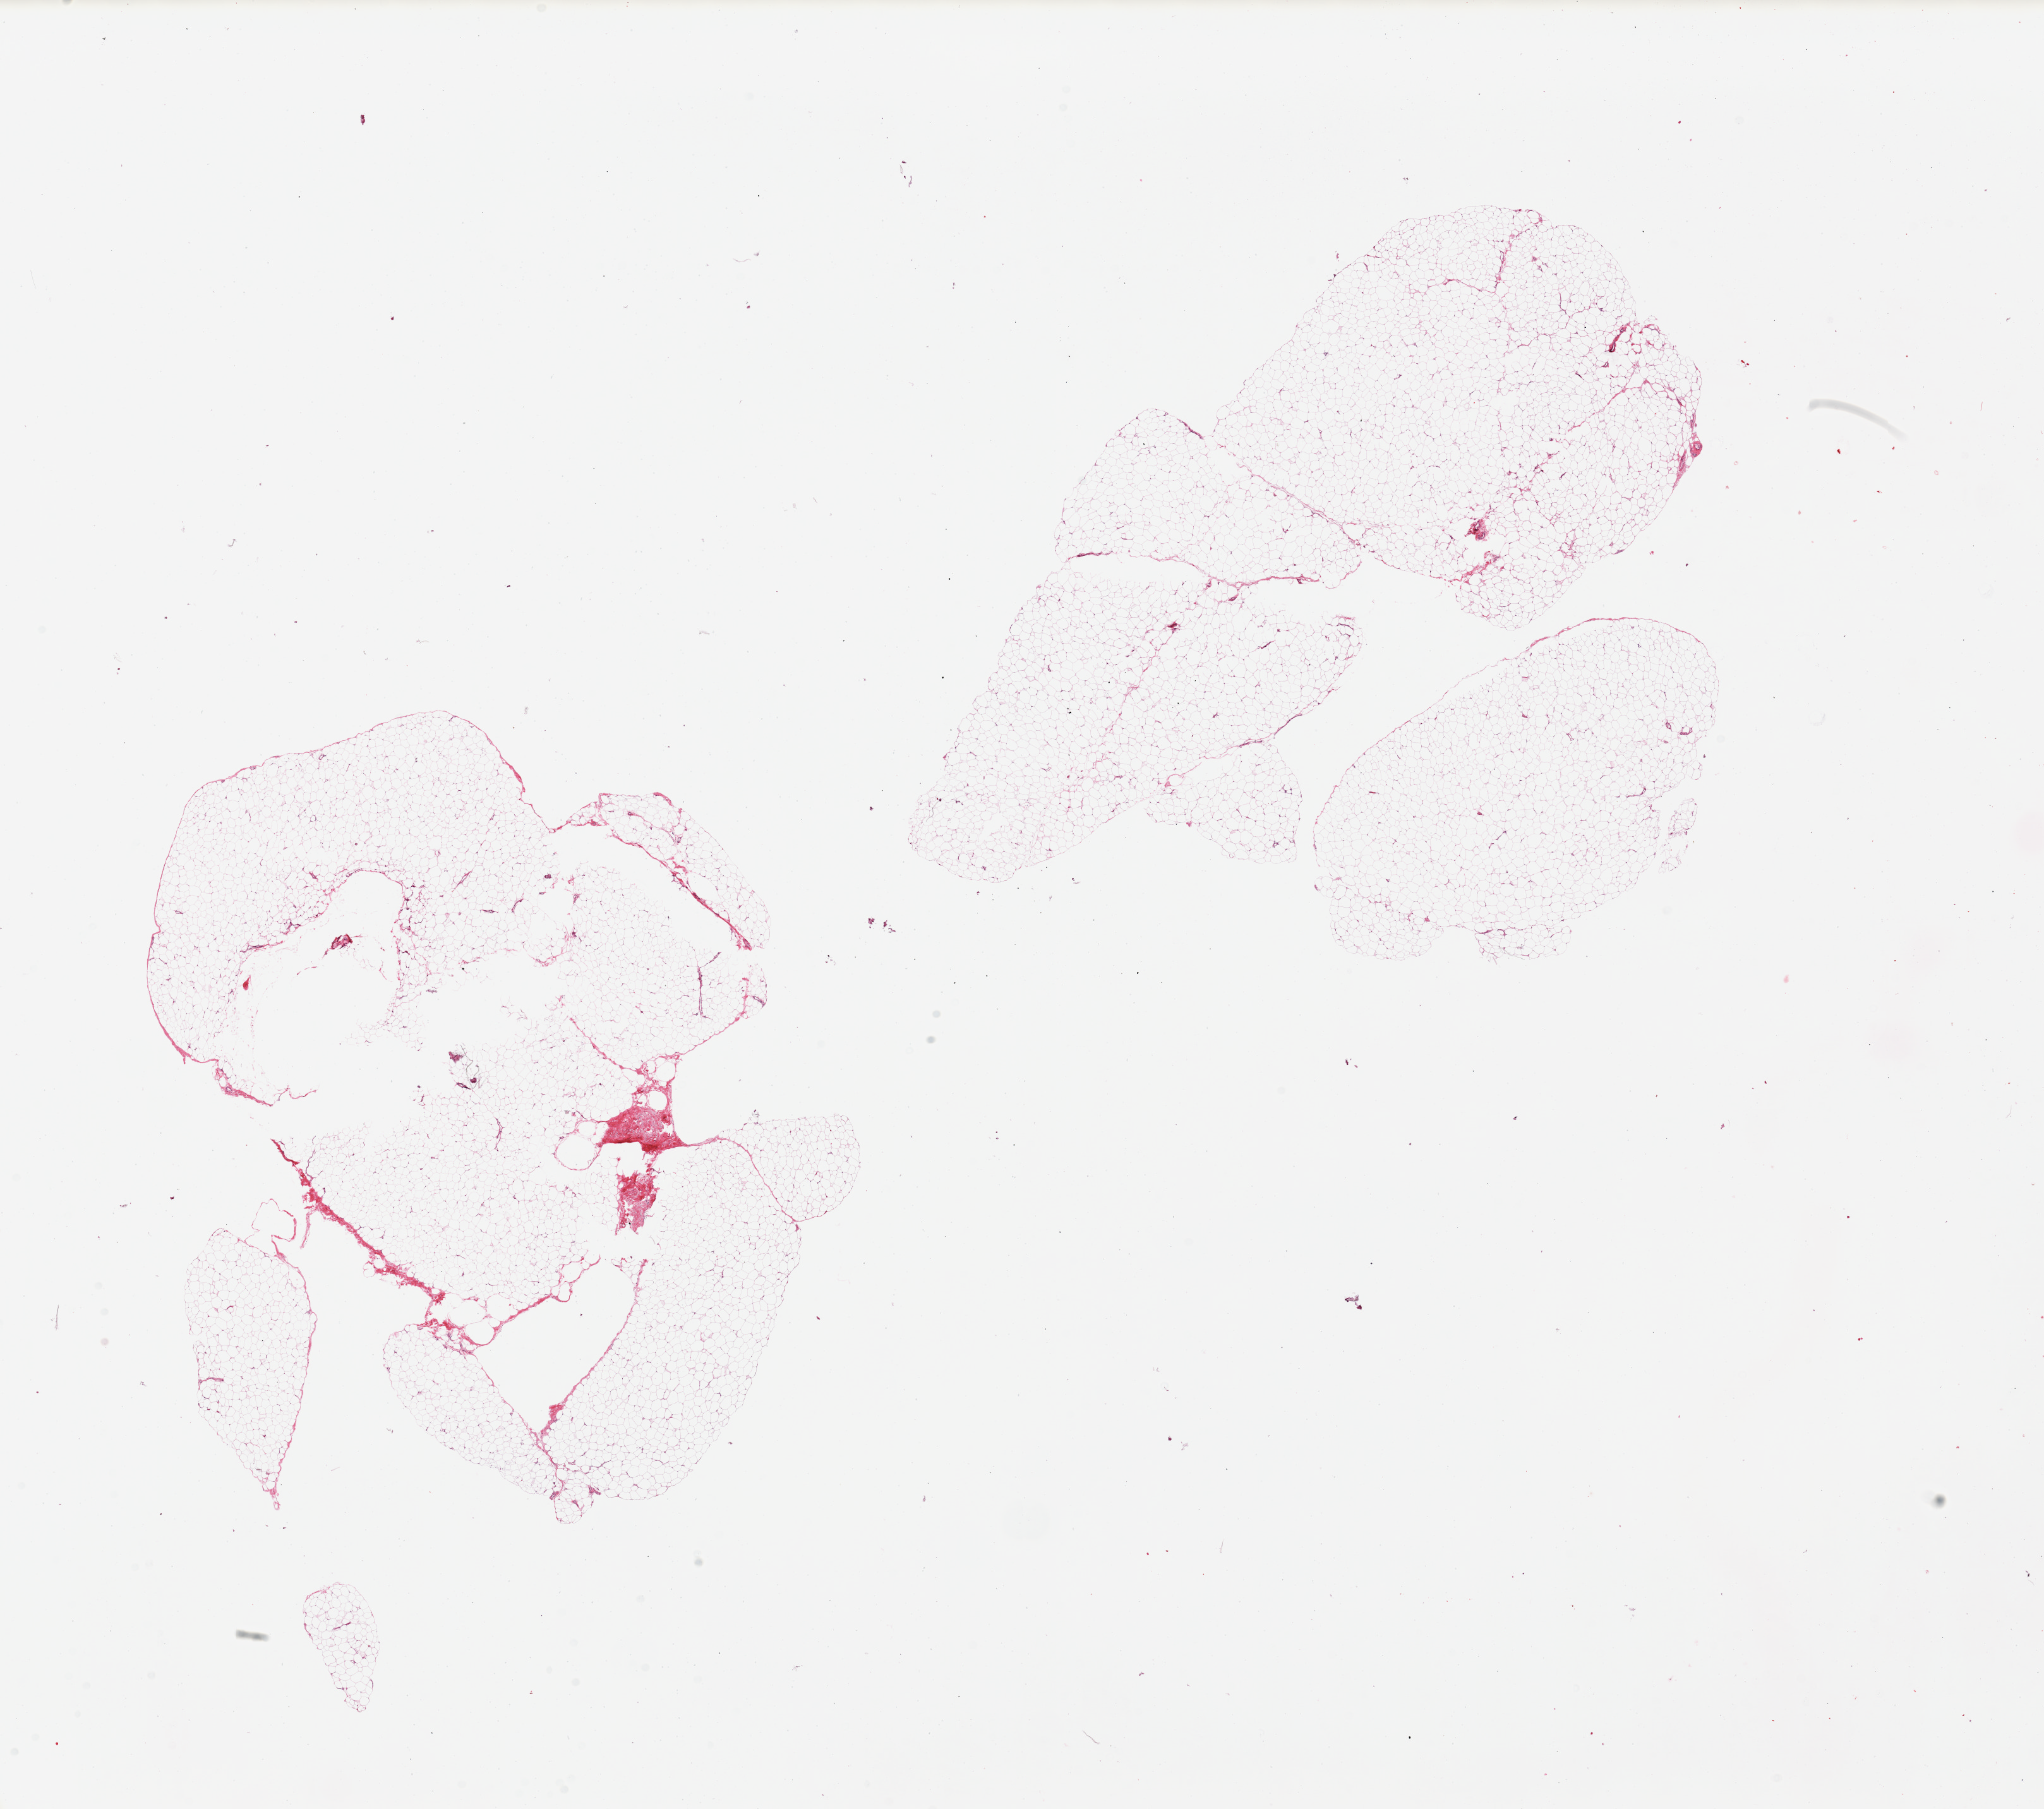
H&E whole-slide image, a low-resolution overview of the entire scanned area, about 25.6 x 22.7 mm (from a 20x scan), PAXgene-fixed paraffin-embedded (PFPE) section, target tissue: adipose tissue, donor tissue sample. Donor sex: male.
Review note (as recorded): 2 pieces. Several internal holes.